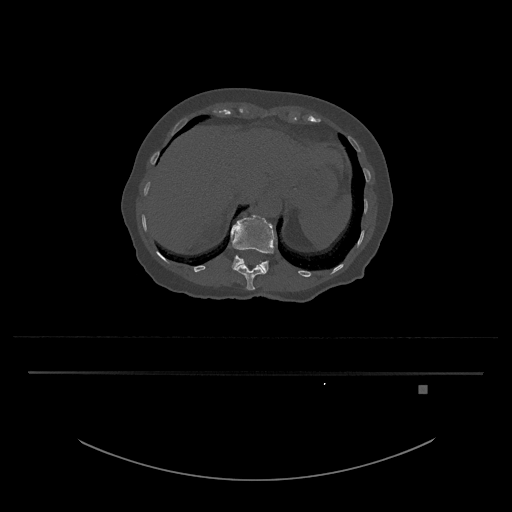
CT including the spine, one axial slice. Slice 584 of 797 in the series (ordered by position). Reconstruction kernel Br40s/3. Bone window (W 1800 / L 400 HU). 0.5 mm slice thickness. 512 × 512 image matrix, field of view 500 × 500 mm. Female patient, age 57 years. Case-level facts recorded for this patient, not image findings: primary cancer: cervical.
Outlined on this slice (semi-automatic segmentation, software-assisted and operator-edited):
- L1 vertebra: bounding box (x1, y1, x2, y2) in pixels: (231, 215, 277, 273)
- T12 vertebra: (235, 262, 265, 290)